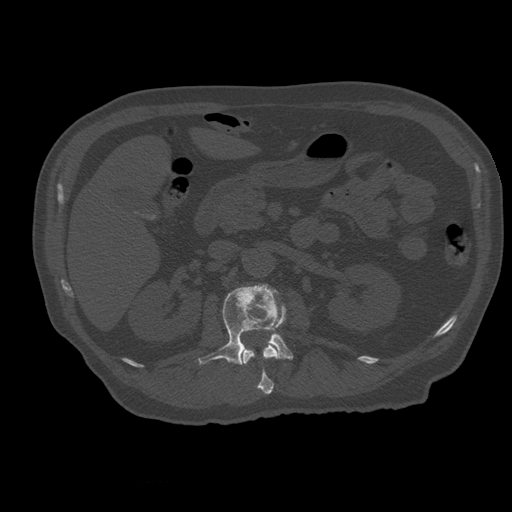
CT including the spine, one axial slice; slice 222 of 399 in the series (ordered by position); reconstruction kernel STANDARD; bone window (W 1800 / L 400 HU); 512 × 512 image matrix, field of view 407 × 407 mm. Patient age 73 years. Case-level facts recorded for this patient, not image findings: primary cancer: prostate; vertebrae with lytic lesions (as recorded): L2.
Annotated regions visible in this slice (semi-automatic segmentation, software-assisted and operator-edited):
- L1 vertebra: bounding box (x1, y1, x2, y2) in pixels: (241, 342, 280, 394)
- L2 vertebra: (199, 284, 293, 365)